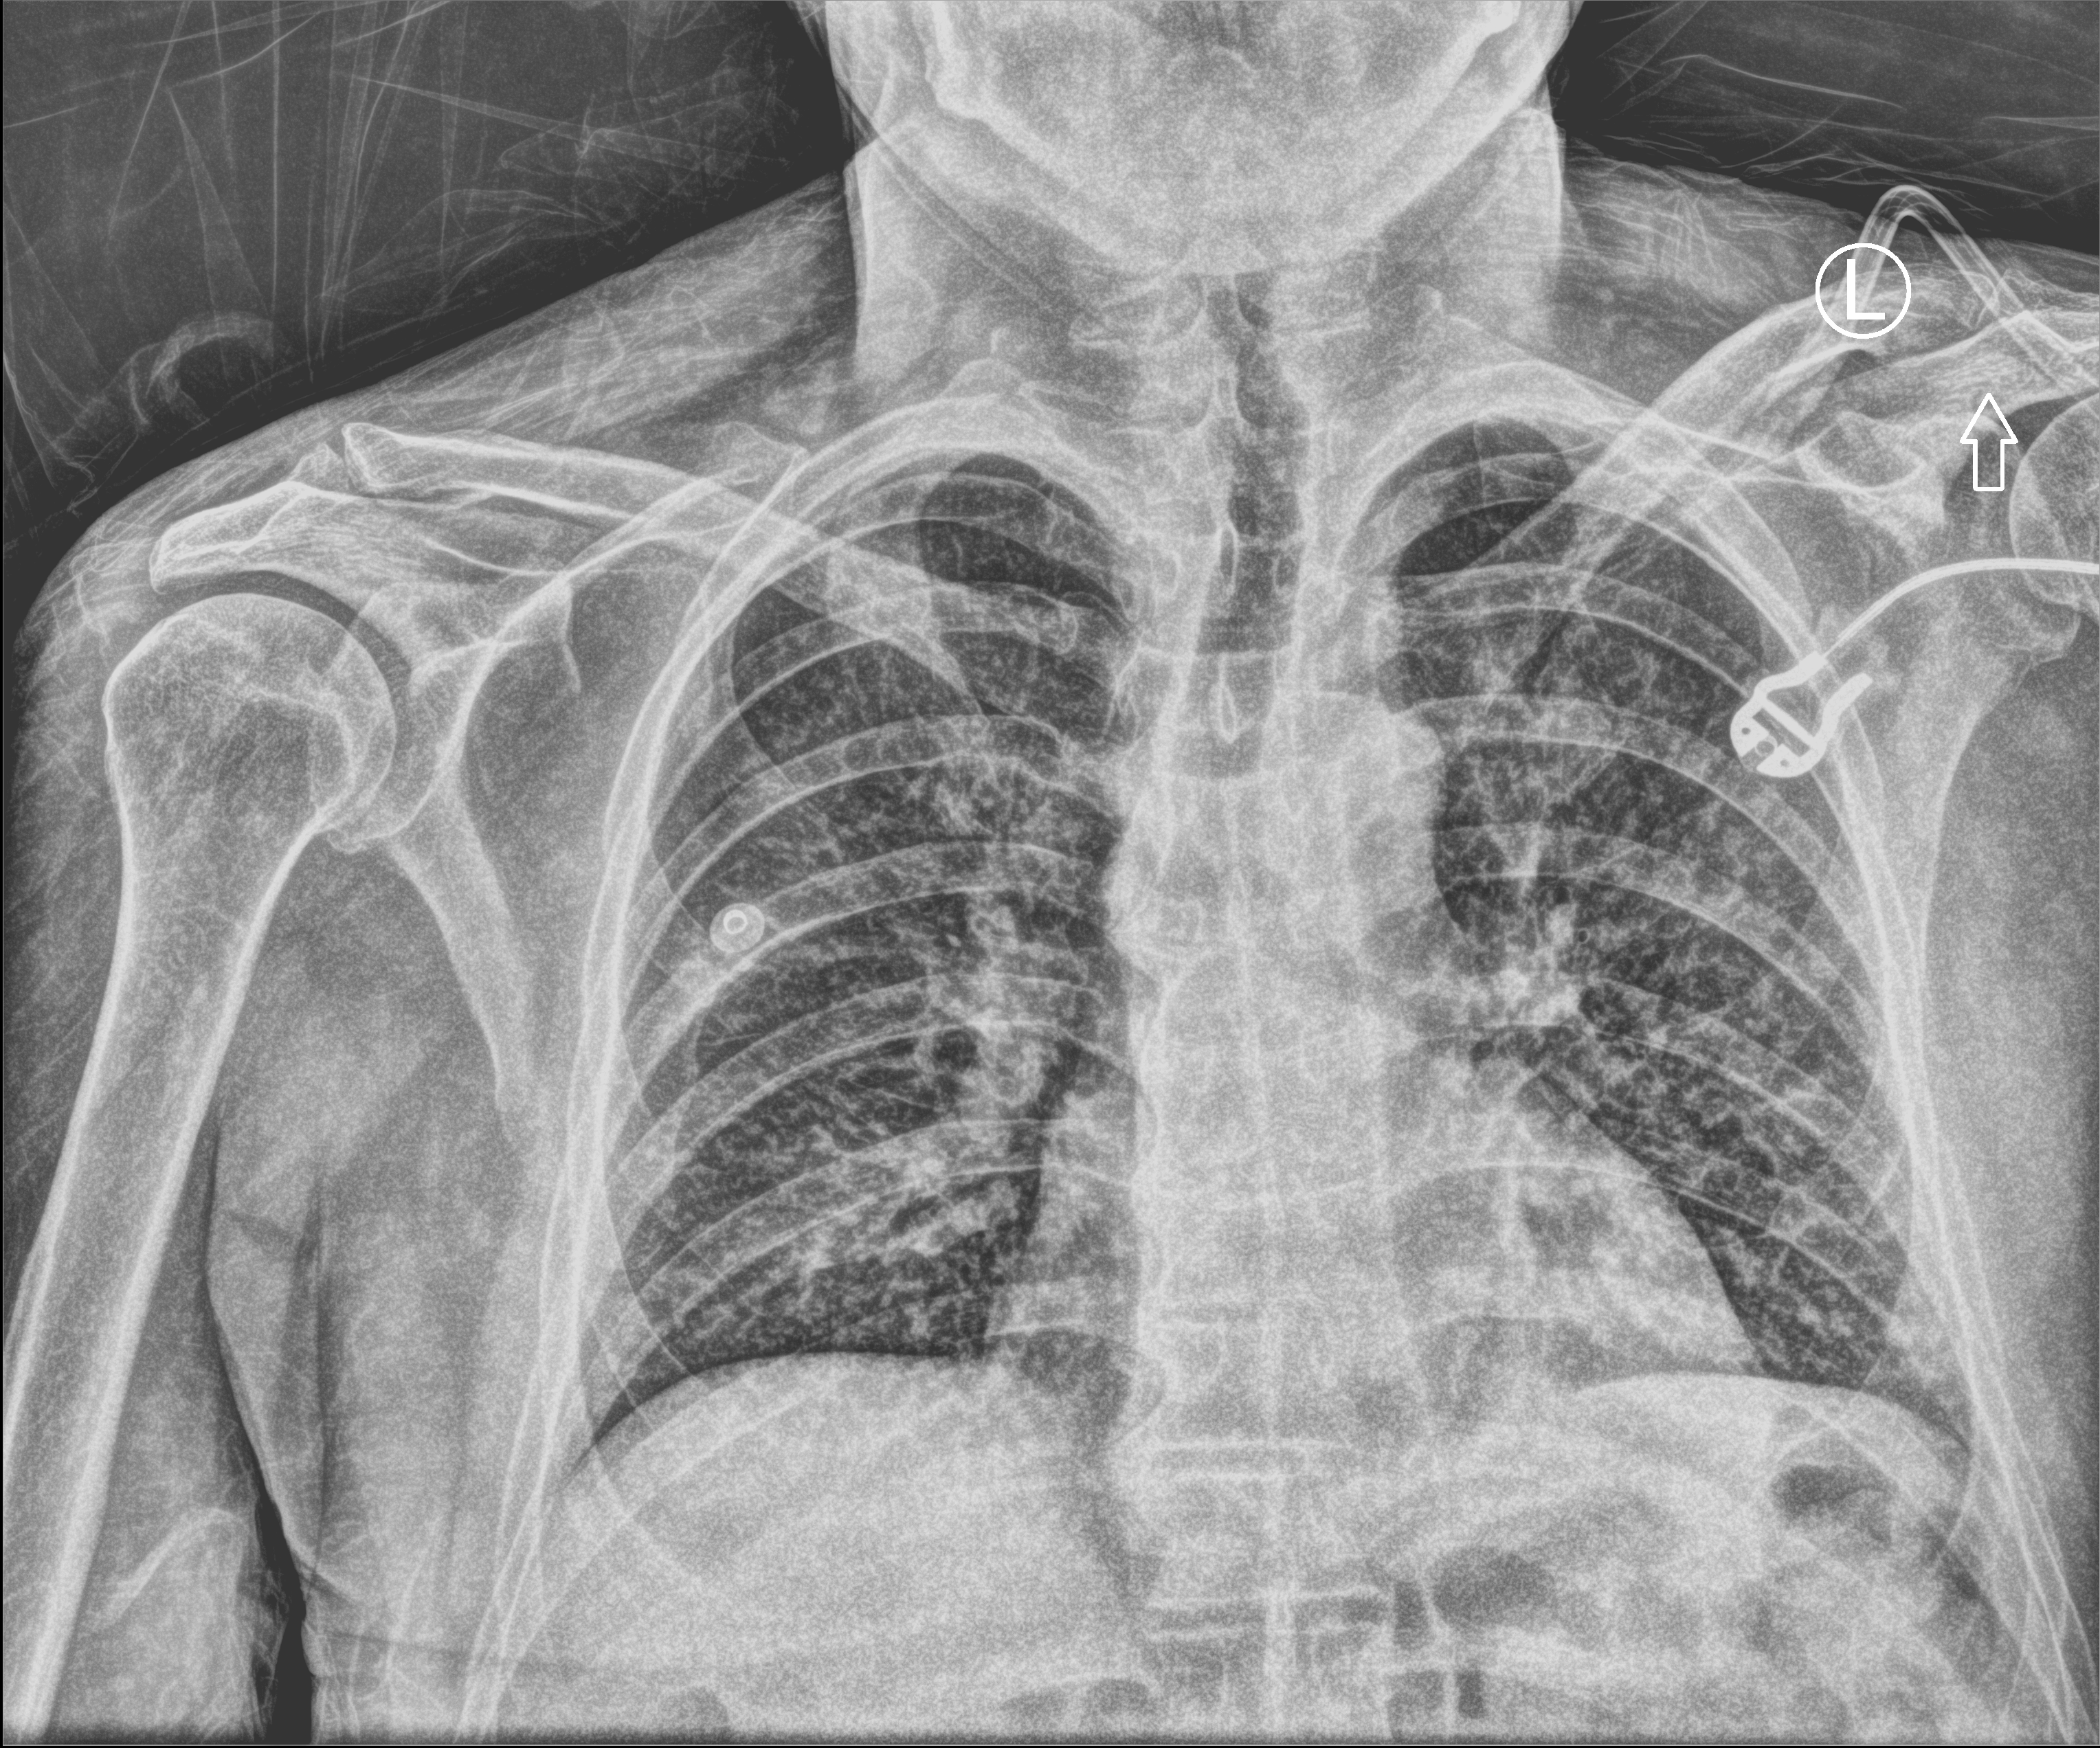
Portable chest radiograph, anteroposterior (AP) projection. Male patient hospitalised with COVID-19, age 18–59 years.
Hospital-stay facts (about this admission, not read from this image; timing relative to this image not recorded): length of hospital stay: 3 days.